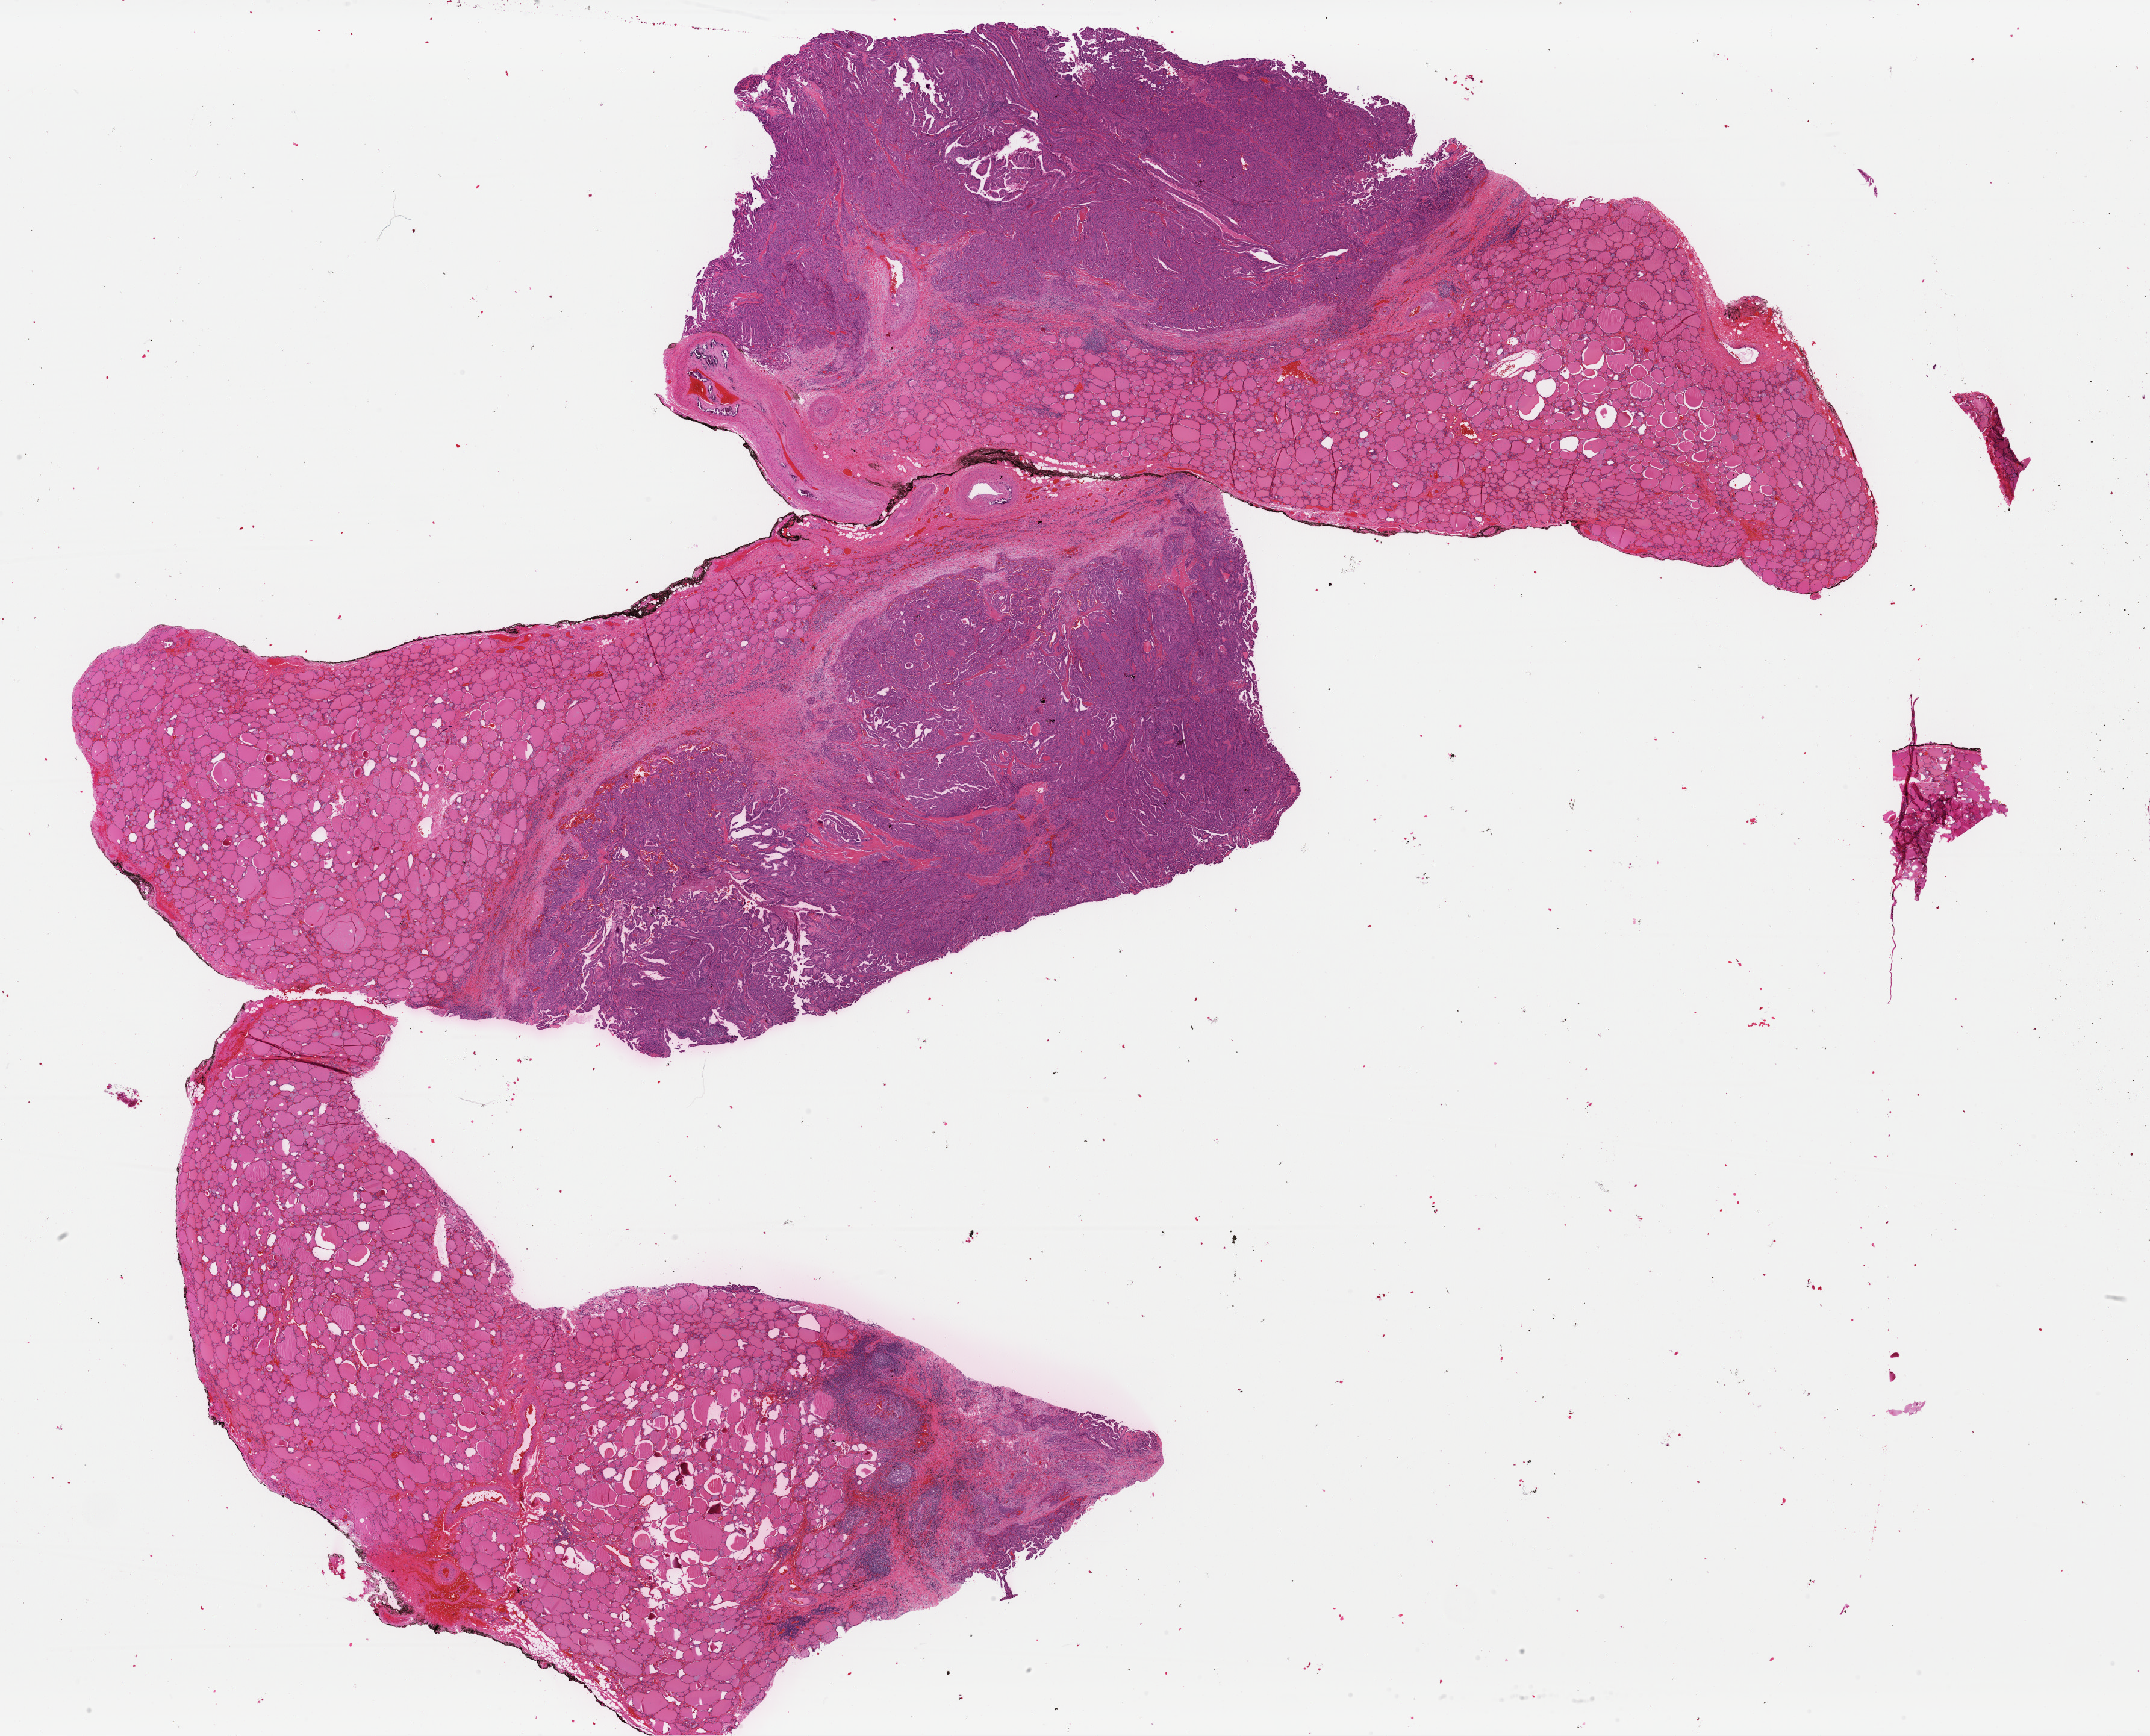
Digitized H&E-stained tissue section (whole slide), low-resolution overview of the scanned area, about 28.2 x 22.8 mm, FFPE section, thyroid, primary tumour sample. Male patient; age at initial diagnosis 64 years.
TNM: T2 N1 MX. AJCC pathologic stage: III. Pathologic diagnosis: Papillary carcinoma, columnar cell (thyroid gland). Lymph nodes positive (case pathology): 1 of 1 examined.